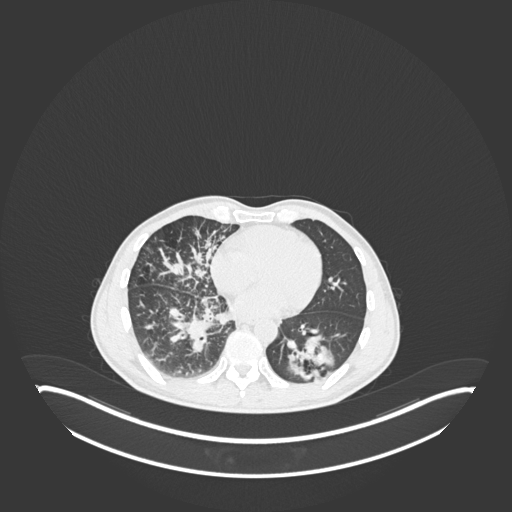
Chest CT, one axial slice; 120 kVp; lung window (W 1500 / L -600 HU); 1 mm slice thickness; 512 × 512 image matrix, field of view 500 × 500 mm. Male patient, age 49 years. Case-level facts recorded for this patient, not image findings: clinical TNM (as recorded): T2b N1 M0.
Outlined on this slice (rectangle marked by the reading radiologist):
- lung tumour (recorded histology: adenocarcinoma): bounding box <283,332,341,383> (left, top, right, bottom; pixels)